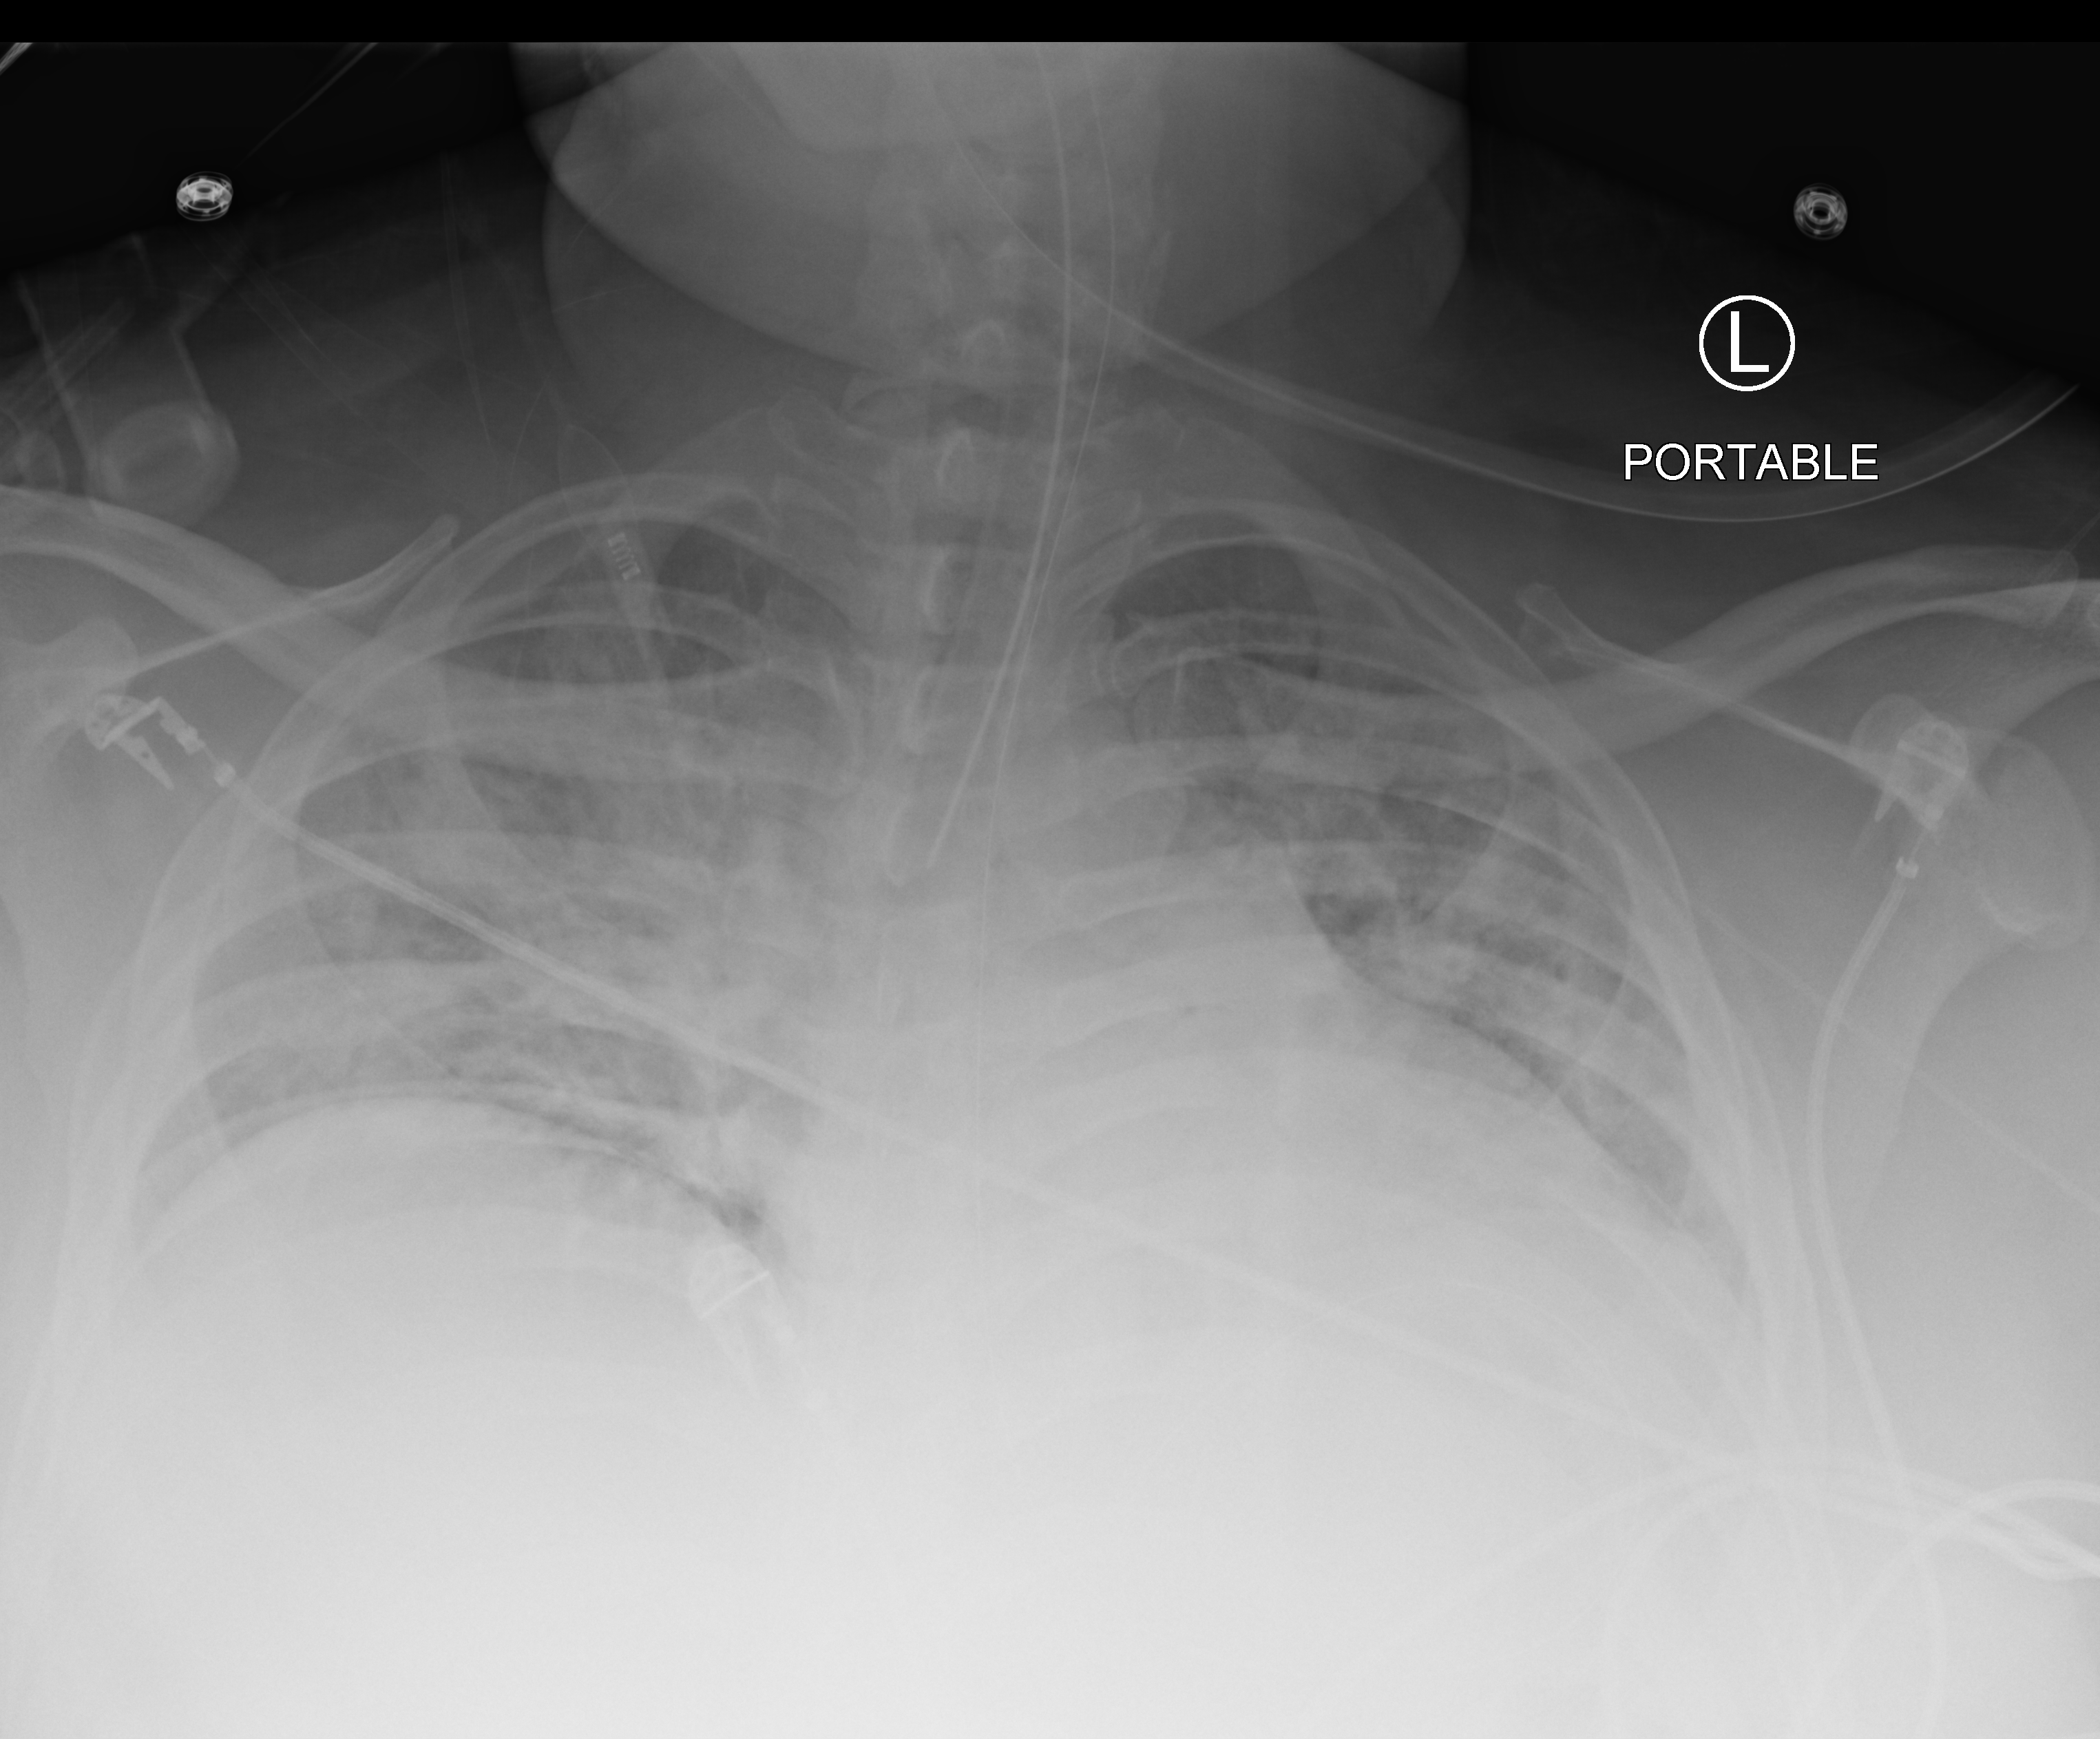
Chest X-ray (portable). Male patient hospitalised with COVID-19, age 18–59 years.
From the hospital-stay record, not from the radiograph (when in the stay this image was taken is not recorded): admitted to intensive care during this hospital stay: yes.